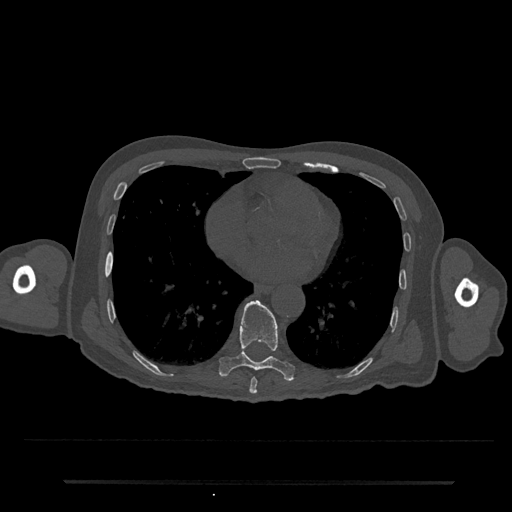
CT including the spine, one axial slice. Slice 372 of 797 in the series (ordered by position). Reconstruction kernel Br40s/3. 120 kVp. Bone window (W 1800 / L 400 HU). 0.5 mm slice thickness. 512 × 512 image matrix, field of view 427 × 427 mm. Patient: male, 74 years. Case-level facts recorded for this patient, not image findings: primary cancer: prostate.
Outlined on this slice (semi-automatically segmented with operator editing):
- T8 vertebra: bounding box [x1, y1, x2, y2] px = [249, 377, 257, 394]
- T9 vertebra: [219, 300, 295, 380]